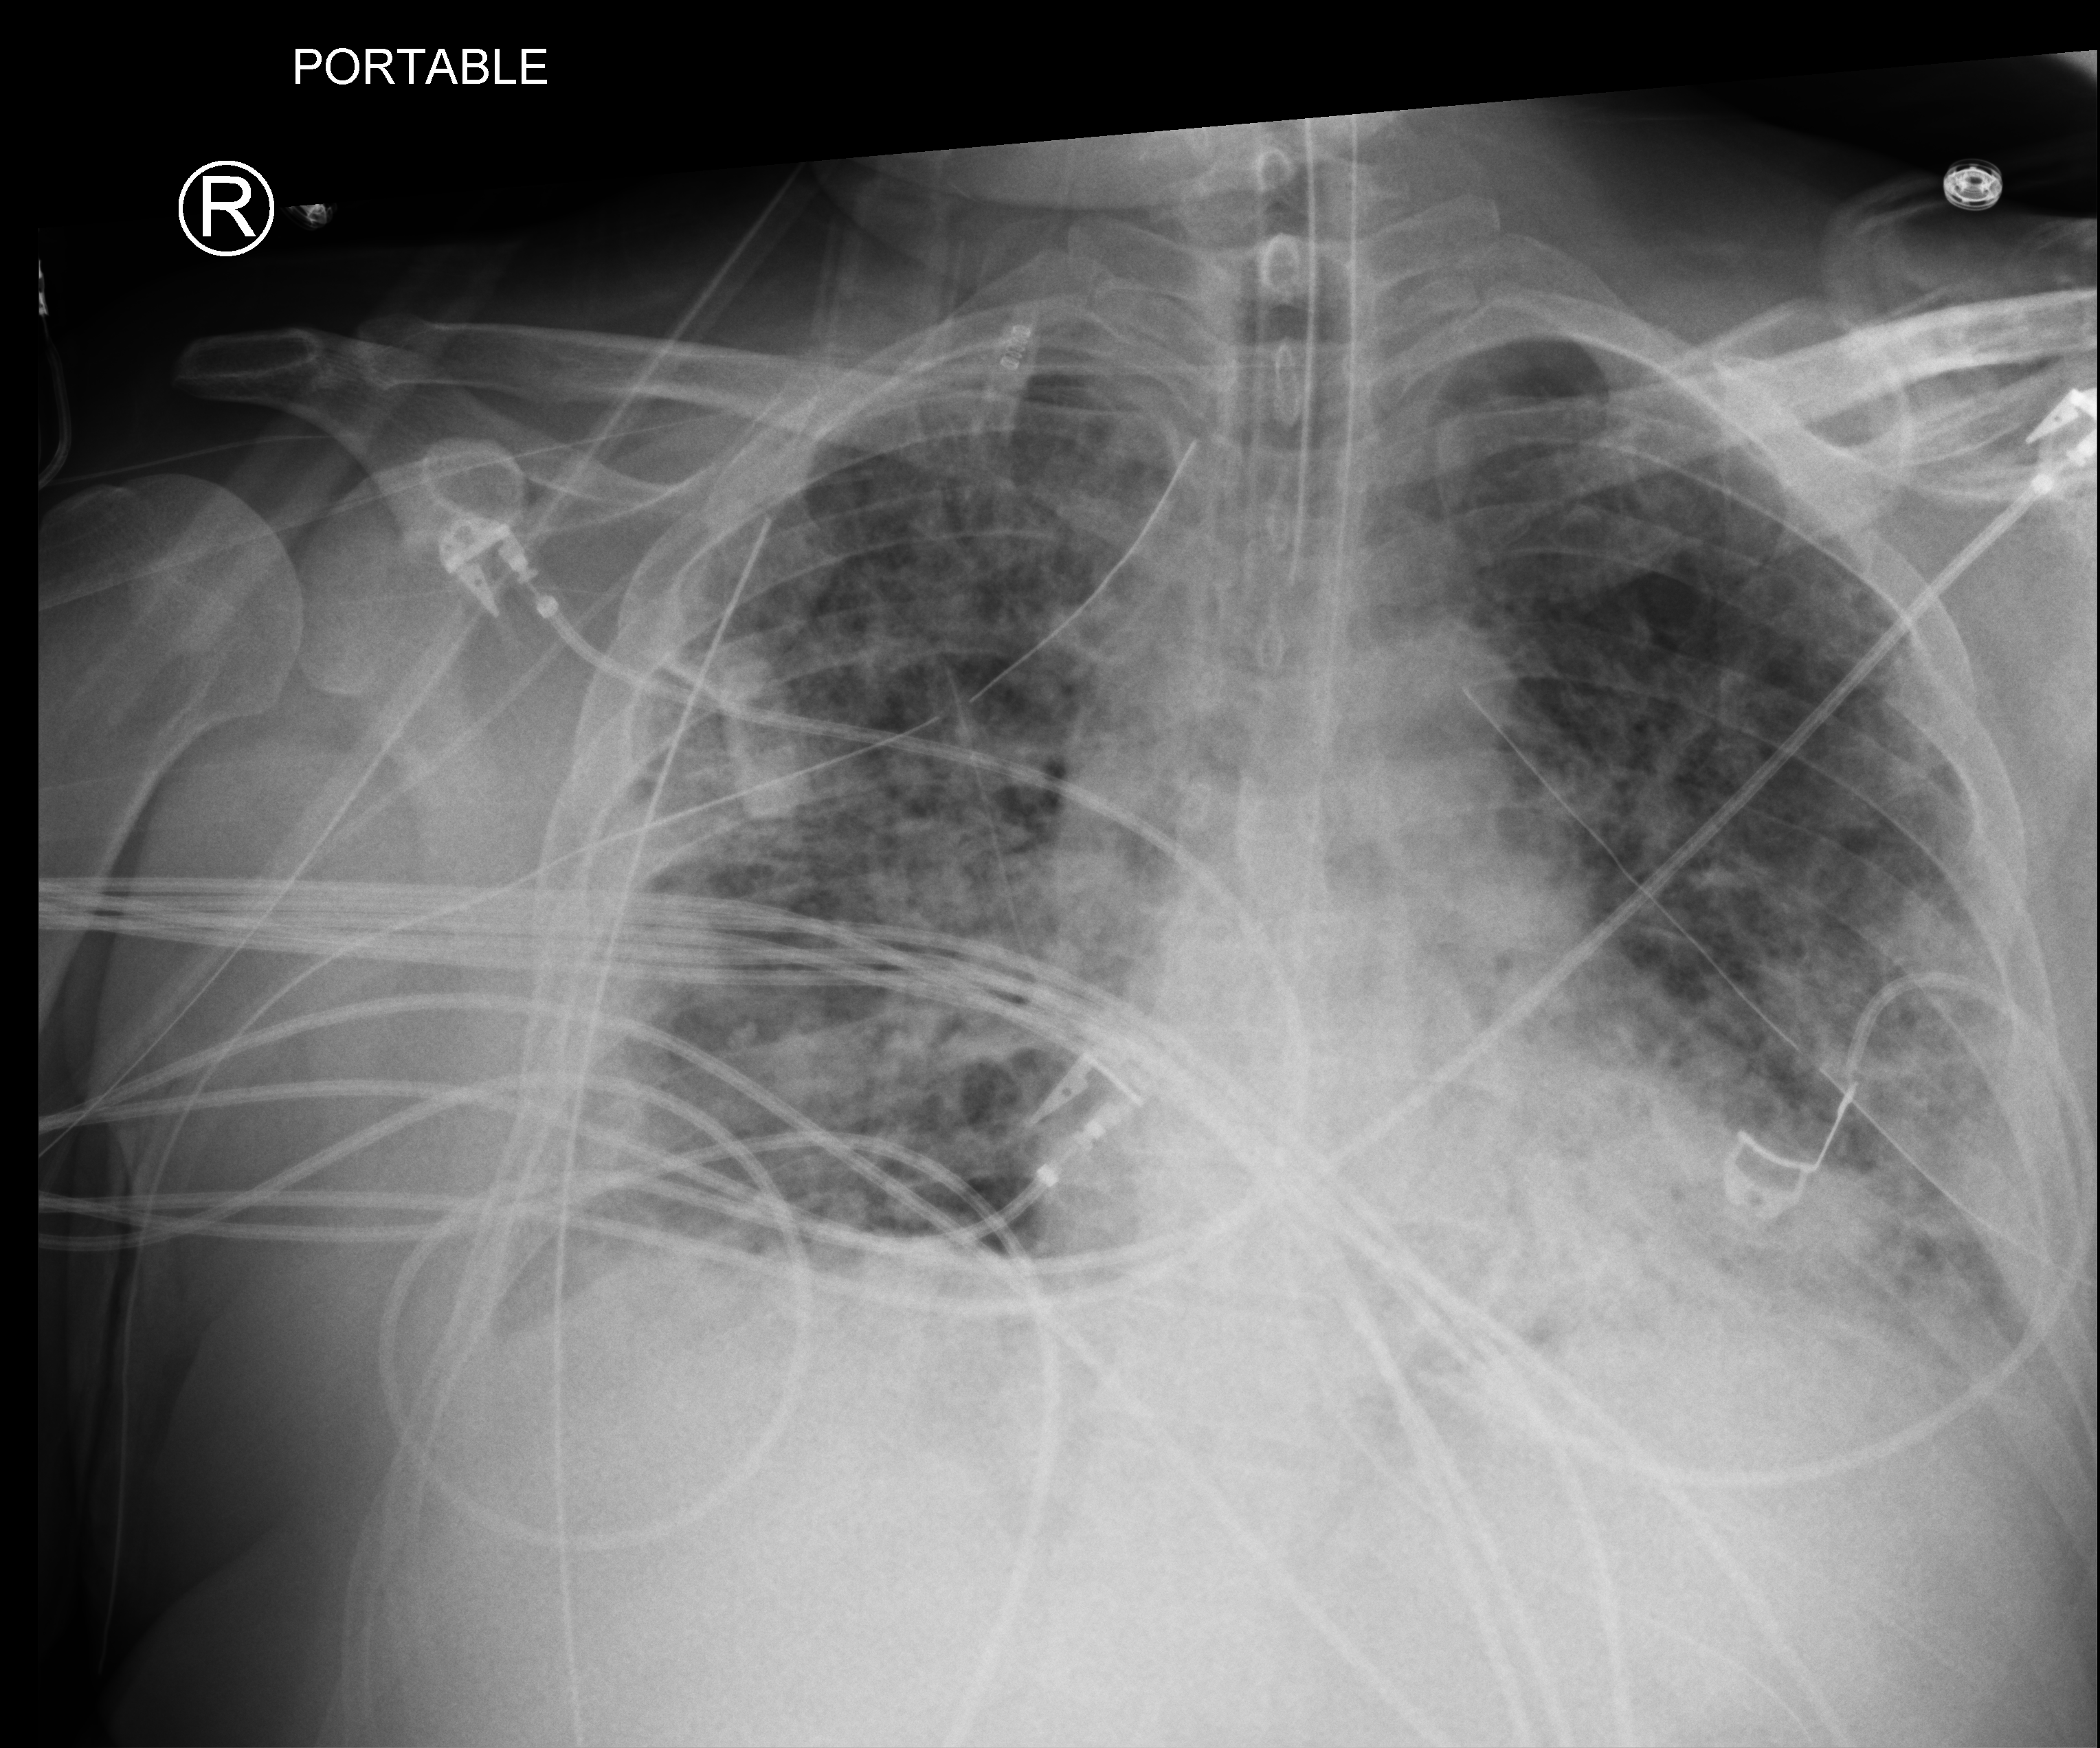
Bedside chest radiograph (computed radiography); anteroposterior (AP) projection. Male patient hospitalised with COVID-19, age 18–59 years.
From the hospital-stay record, not from the radiograph (when in the stay this image was taken is not recorded):
- mechanically ventilated during this hospital stay: yes